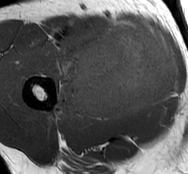
MRI of an extremity soft-tissue mass, one axial slice; position 39 of 93 along the scan axis; MR volume resampled by the dataset authors to the PET/CT grid (not the native acquisition matrix); 3.27 mm slice thickness; 188 × 174 image matrix, field of view 184 × 170 mm. Male patient. Case-level facts recorded for this patient, not image findings: histological type: undifferentiated - pleiomorphic; grade: high; site of the primary tumour: right thigh.
Outlined on this slice (expert contour drawn on MRI and transferred to this co-registered scan by the dataset authors):
- gross tumour volume including surrounding oedema: bounding box [x1, y1, x2, y2] px = [54, 21, 180, 121]
- gross tumour volume (mass): [70, 23, 178, 118]